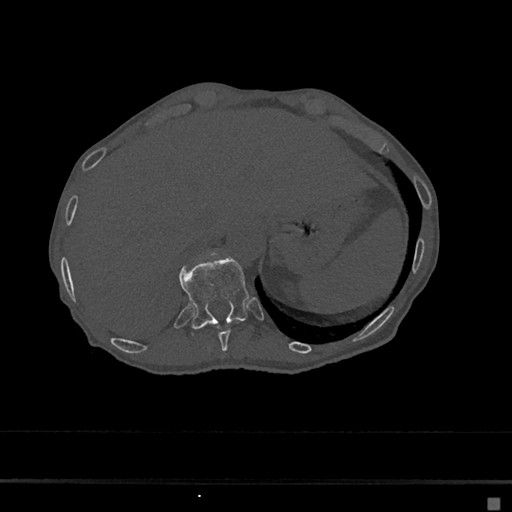
CT including the spine, one axial slice. Slice 187 of 797 in the series (ordered by position). Reconstruction kernel Br40s/3. Bone window (W 1800 / L 400 HU). 0.5 mm slice thickness. 512 × 512 image matrix, field of view 360 × 360 mm. Patient: female, 68 years. Case-level facts recorded for this patient, not image findings: primary cancer: renal.
Structures marked on this image (semi-automatic segmentation, software-assisted and operator-edited):
- T10 vertebra: box from (x=216, y=321) to (x=240, y=352) px
- T11 vertebra: (x=180, y=257)–(x=249, y=329)